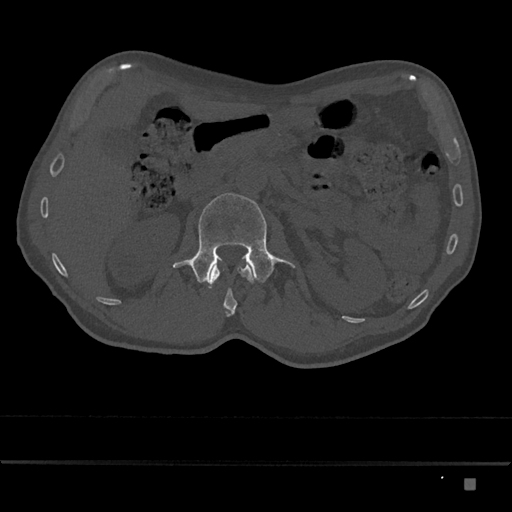
CT including the spine, one axial slice; slice 498 of 797 in the series (ordered by position); 120 kVp; bone window (W 1800 / L 400 HU); 0.5 mm slice thickness; 512 × 512 image matrix, field of view 390 × 390 mm. Male patient, age 72 years. Case-level facts recorded for this patient, not image findings: primary cancer: prostate.
Outlined on this slice (semi-automatic segmentation, software-assisted and operator-edited):
- L1 vertebra: bounding box <208,258,254,317> (left, top, right, bottom; pixels)
- L2 vertebra: <173,193,296,284>